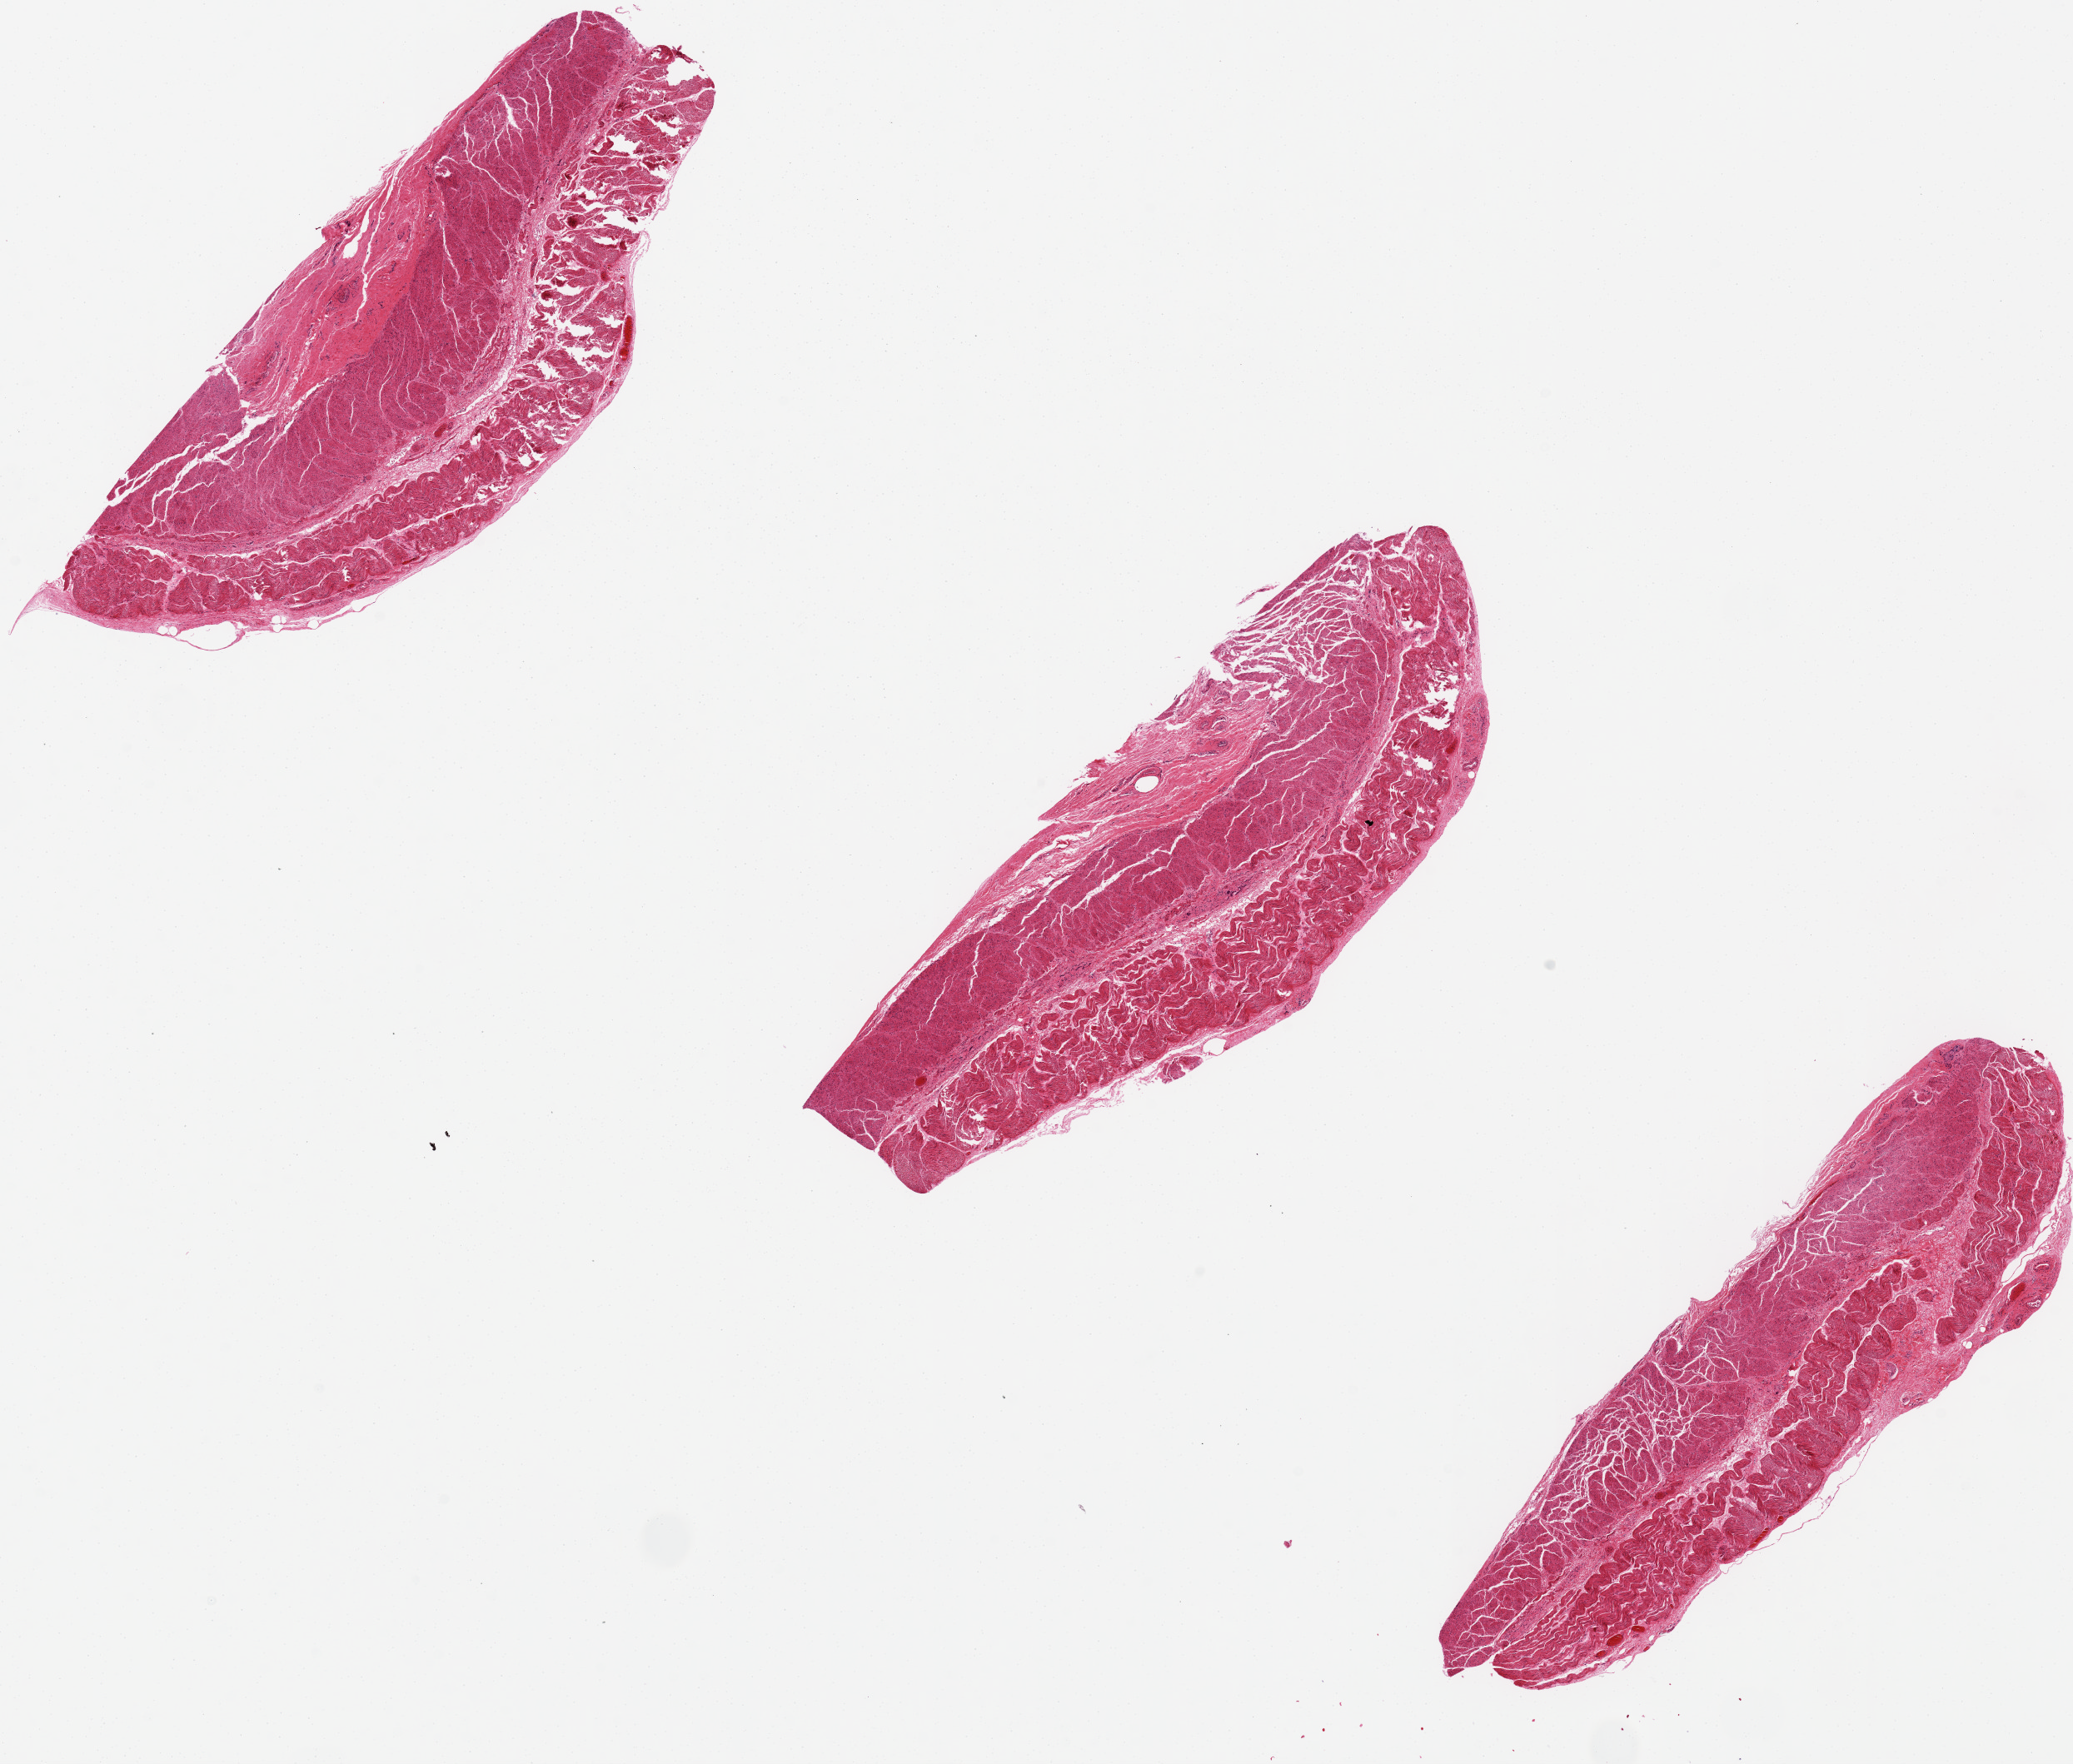
H&E whole-slide image — low-resolution overview of the scanned area, about 19.7 x 16.8 mm (acquisition: 20x scan); PAXgene-fixed paraffin-embedded (PFPE) section; sampled site (target tissue): esophageal muscle; tissue donor sample. Donor sex: male.
Reviewer comment on this tissue sample: 3 ~8x3.5mm pieces of fibro connective tissue, uncertain provenance.